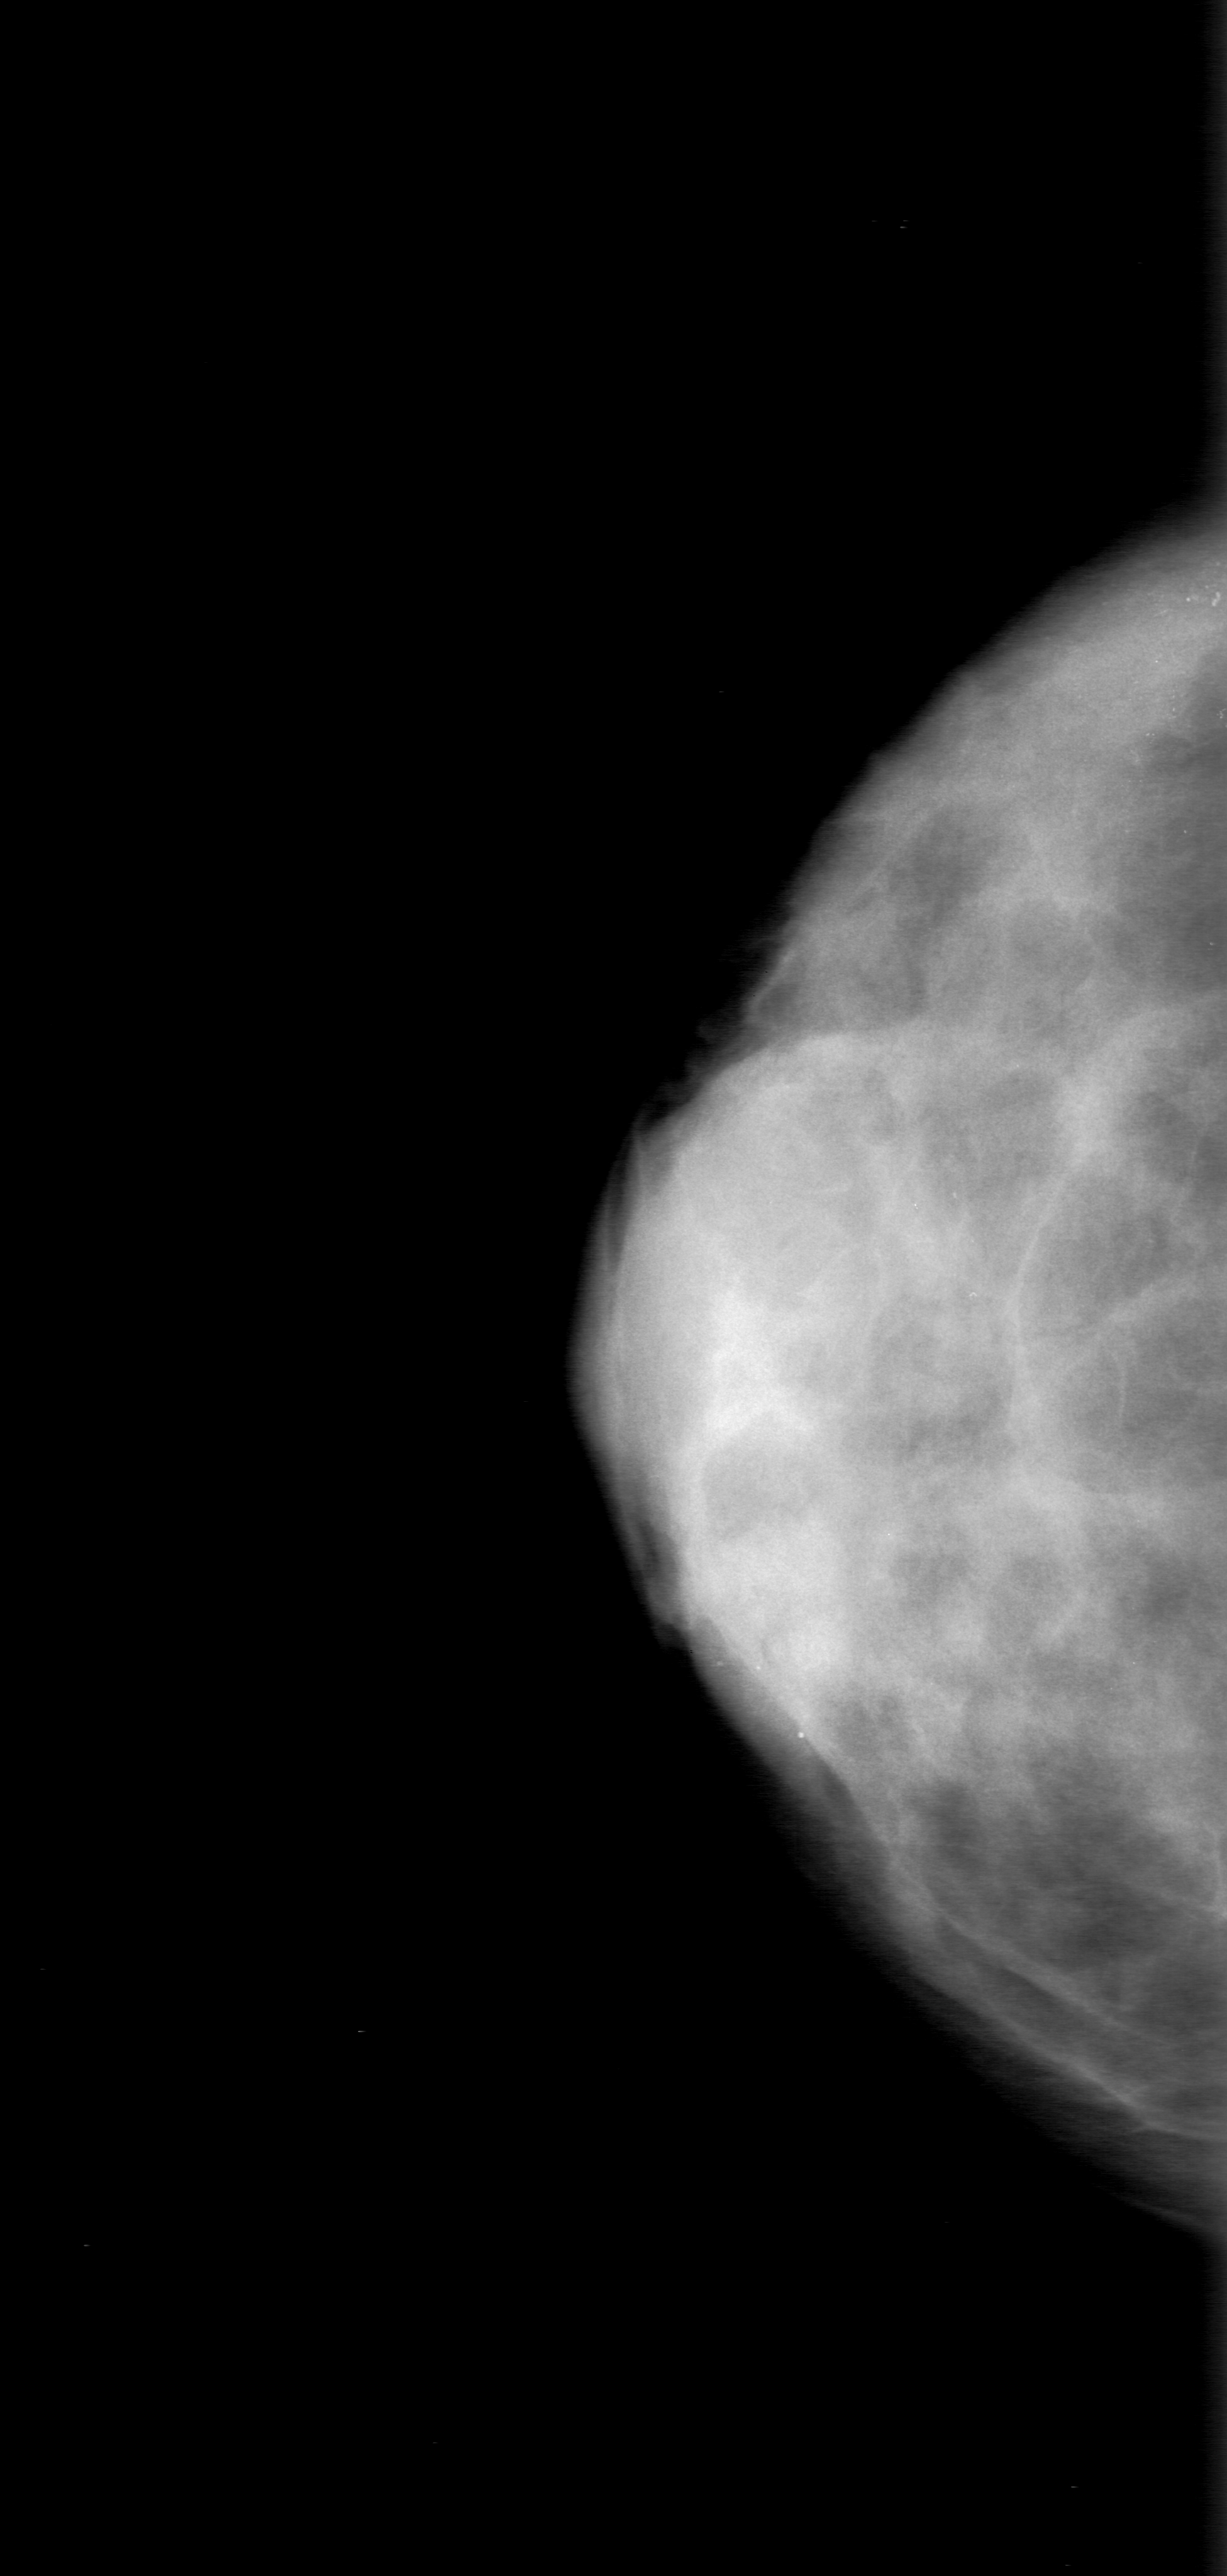
Mammogram (digitized film). Right breast. CC view. 1227 × 2576 image matrix.
Marked abnormalities (boxes around the expert regions of interest):
- calcifications, morphology pleomorphic, distribution clustered; BI-RADS assessment category 3; subtlety rating 2 on a 1 (subtle) to 5 (obvious) scale; pathology result (as recorded, not read from the image): malignant: box from (x=1081, y=512) to (x=1216, y=700) px